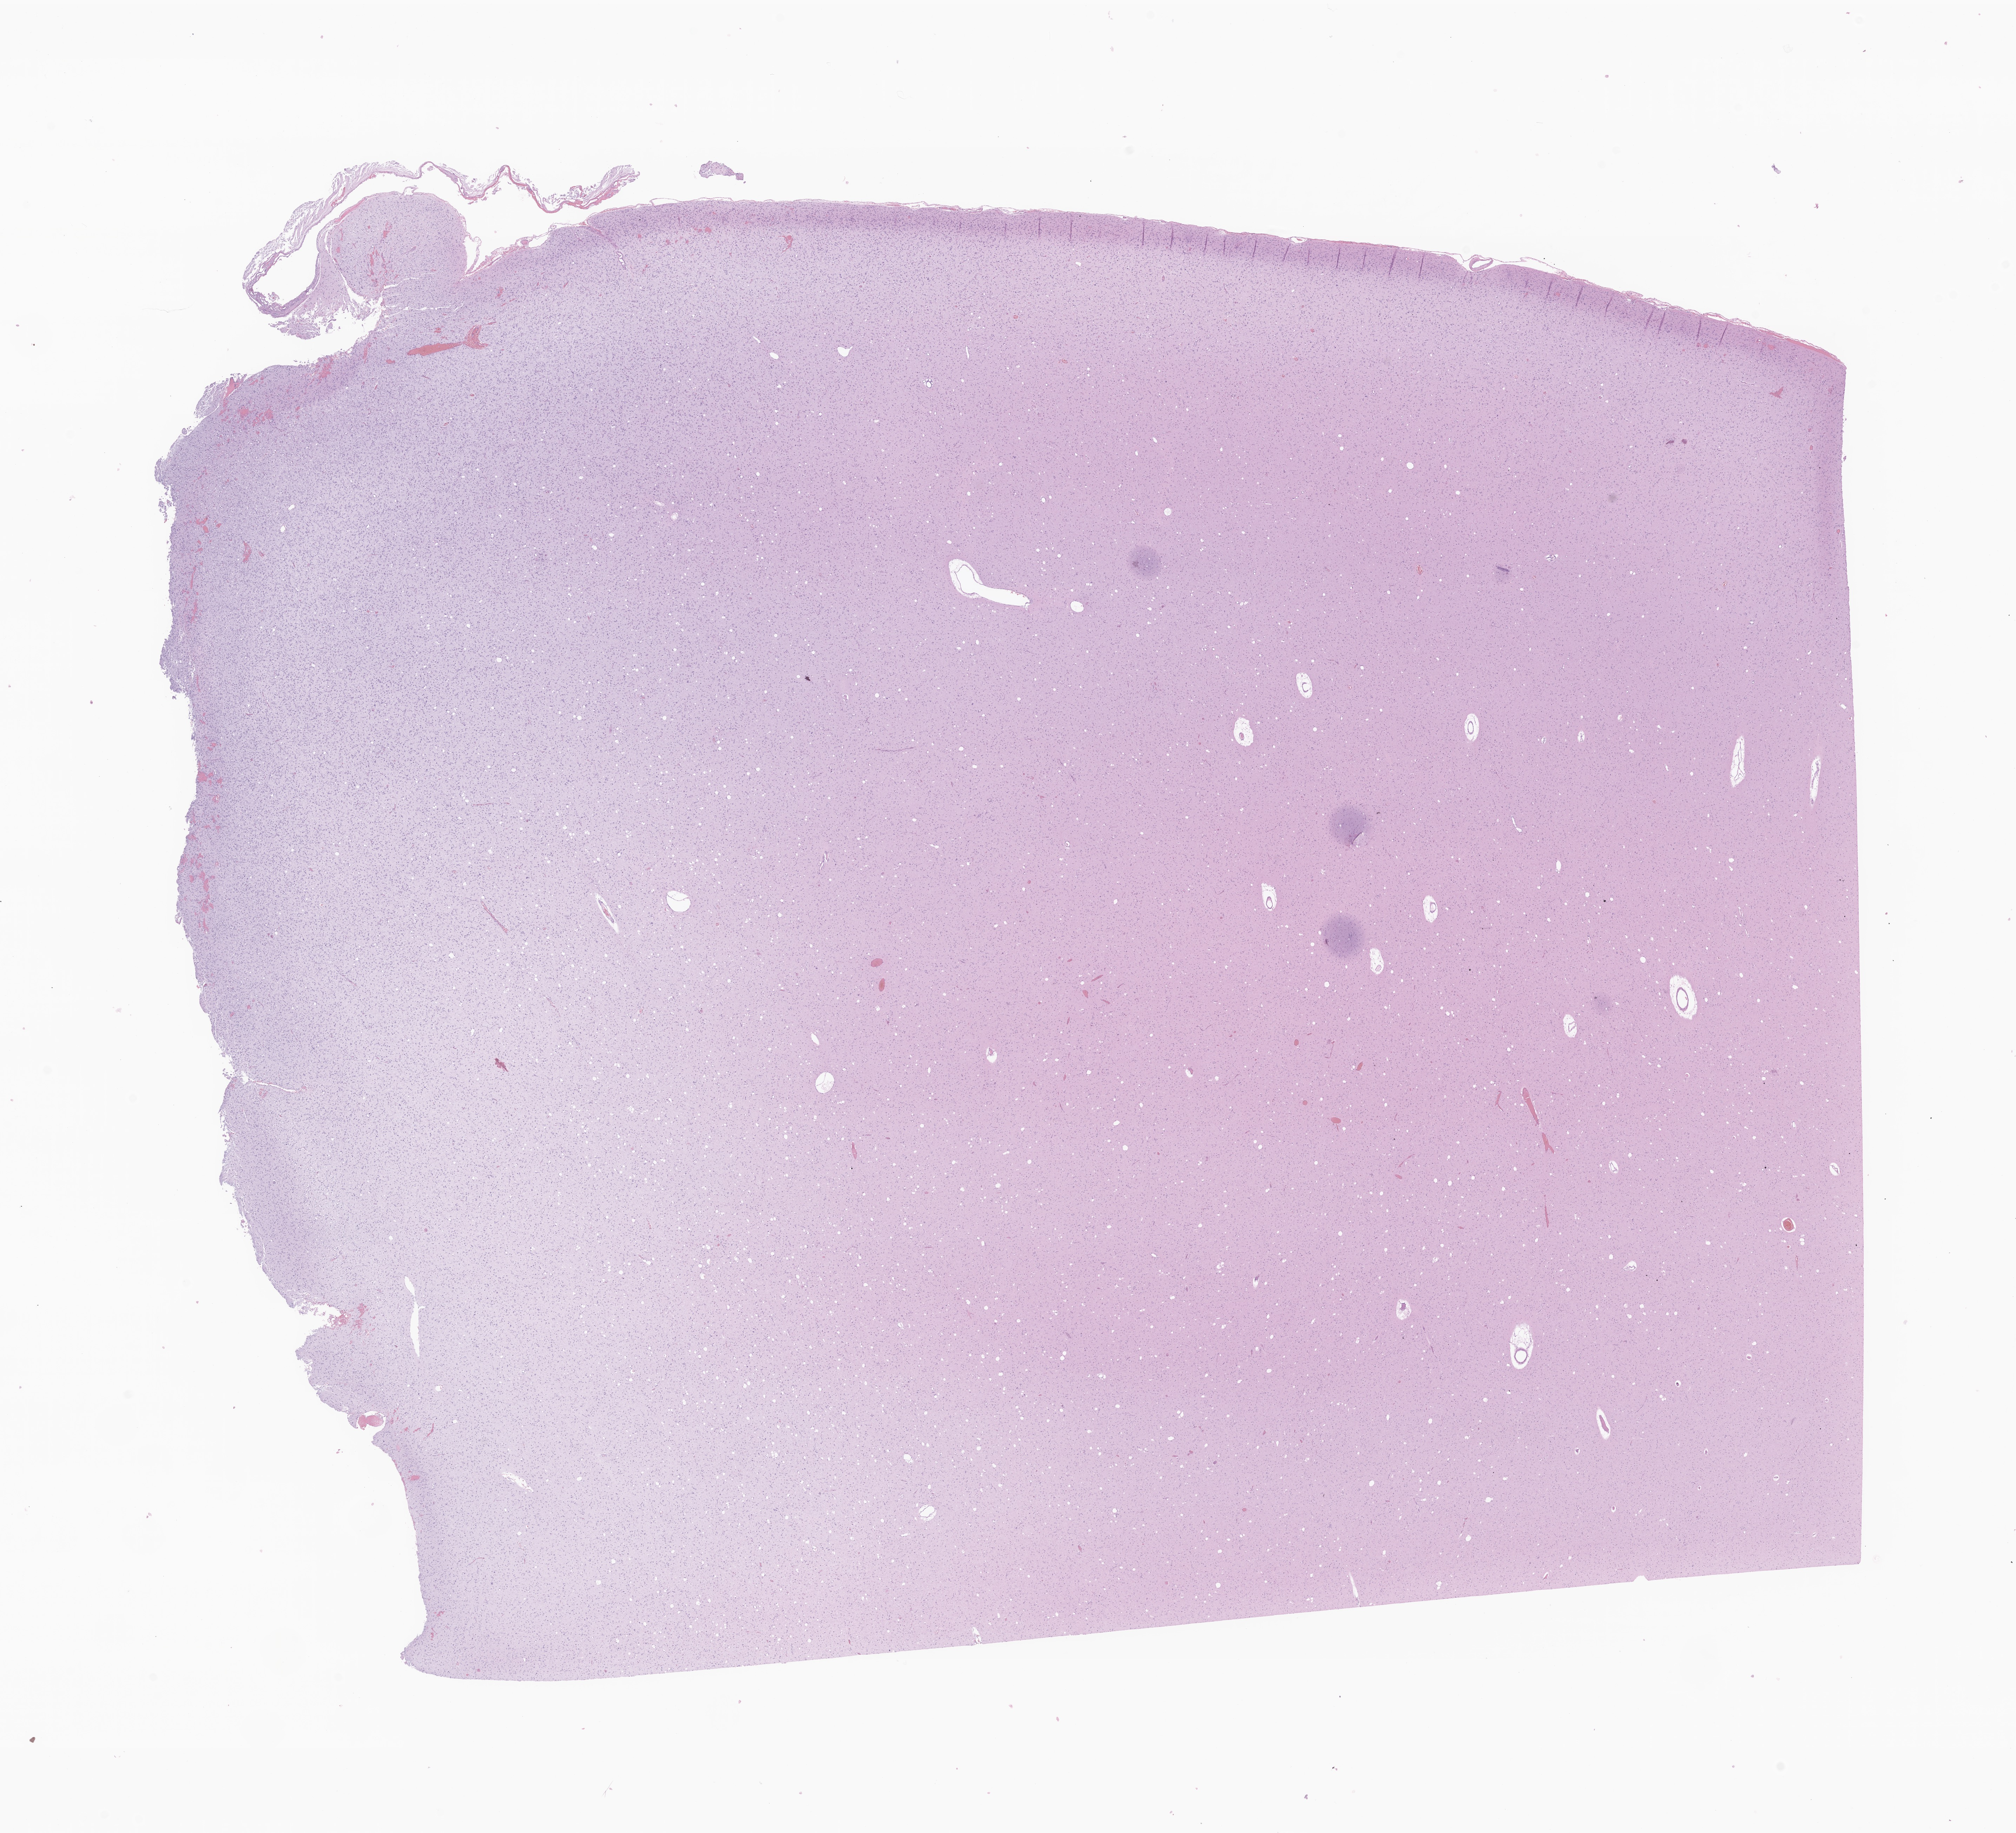
Whole-slide image, H&E stain of tumor tissue from the brain, whole scanned area (about 24.2 x 22.0 mm) shown as a low-resolution overview; formalin-fixed, paraffin-embedded (FFPE) tissue. Patient female; age 172 months (14 years 4 months).
Diagnosis (ICD-O-3 morphology term): Astrocytoma, anaplastic, NOS.